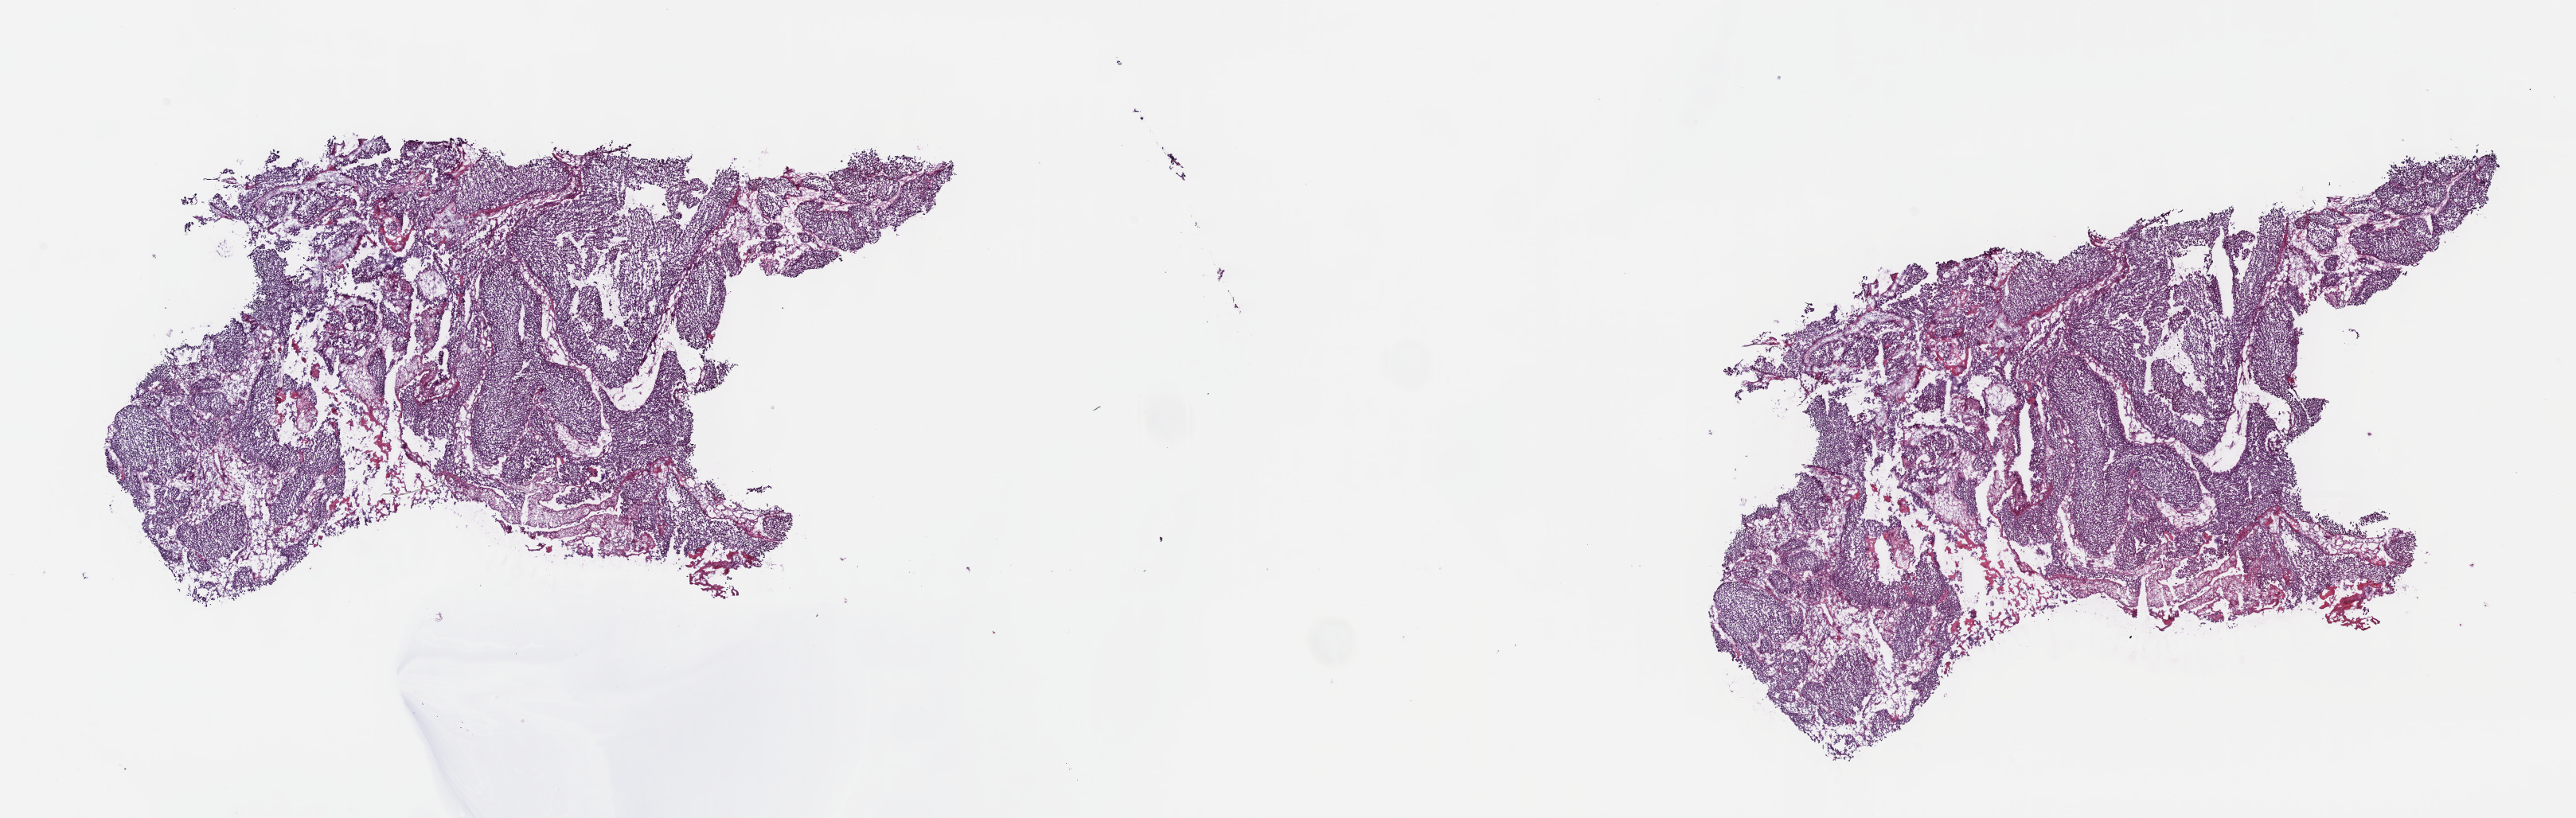
H&E-stained whole-slide image, shown as a low-resolution overview of the whole scanned area (about 26.2 x 8.3 mm, acquisition: 40x scan); frozen section from the top of the tissue portion; primary tumour sample from the bladder. Patient: male, age at initial diagnosis 52 years.
Diagnosis: Papillary transitional cell carcinoma.